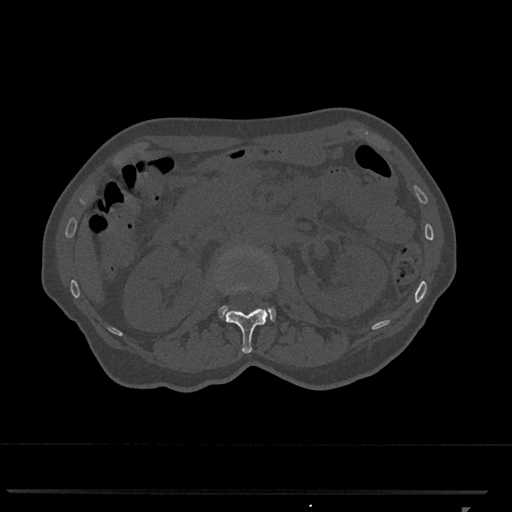
CT including the spine, one axial slice; slice 379 of 793 in the series (ordered by position); 120 kVp; bone window (W 1800 / L 400 HU); 0.5 mm slice thickness; 512 × 512 image matrix. Female patient, age 62 years. From the clinical record (not read from this slice): primary cancer: renal.
Outlined on this slice (semi-automatic segmentation, software-assisted and operator-edited):
- L1 vertebra: bounding box <225,285,267,354> (left, top, right, bottom; pixels)
- L2 vertebra: <218,251,276,322>